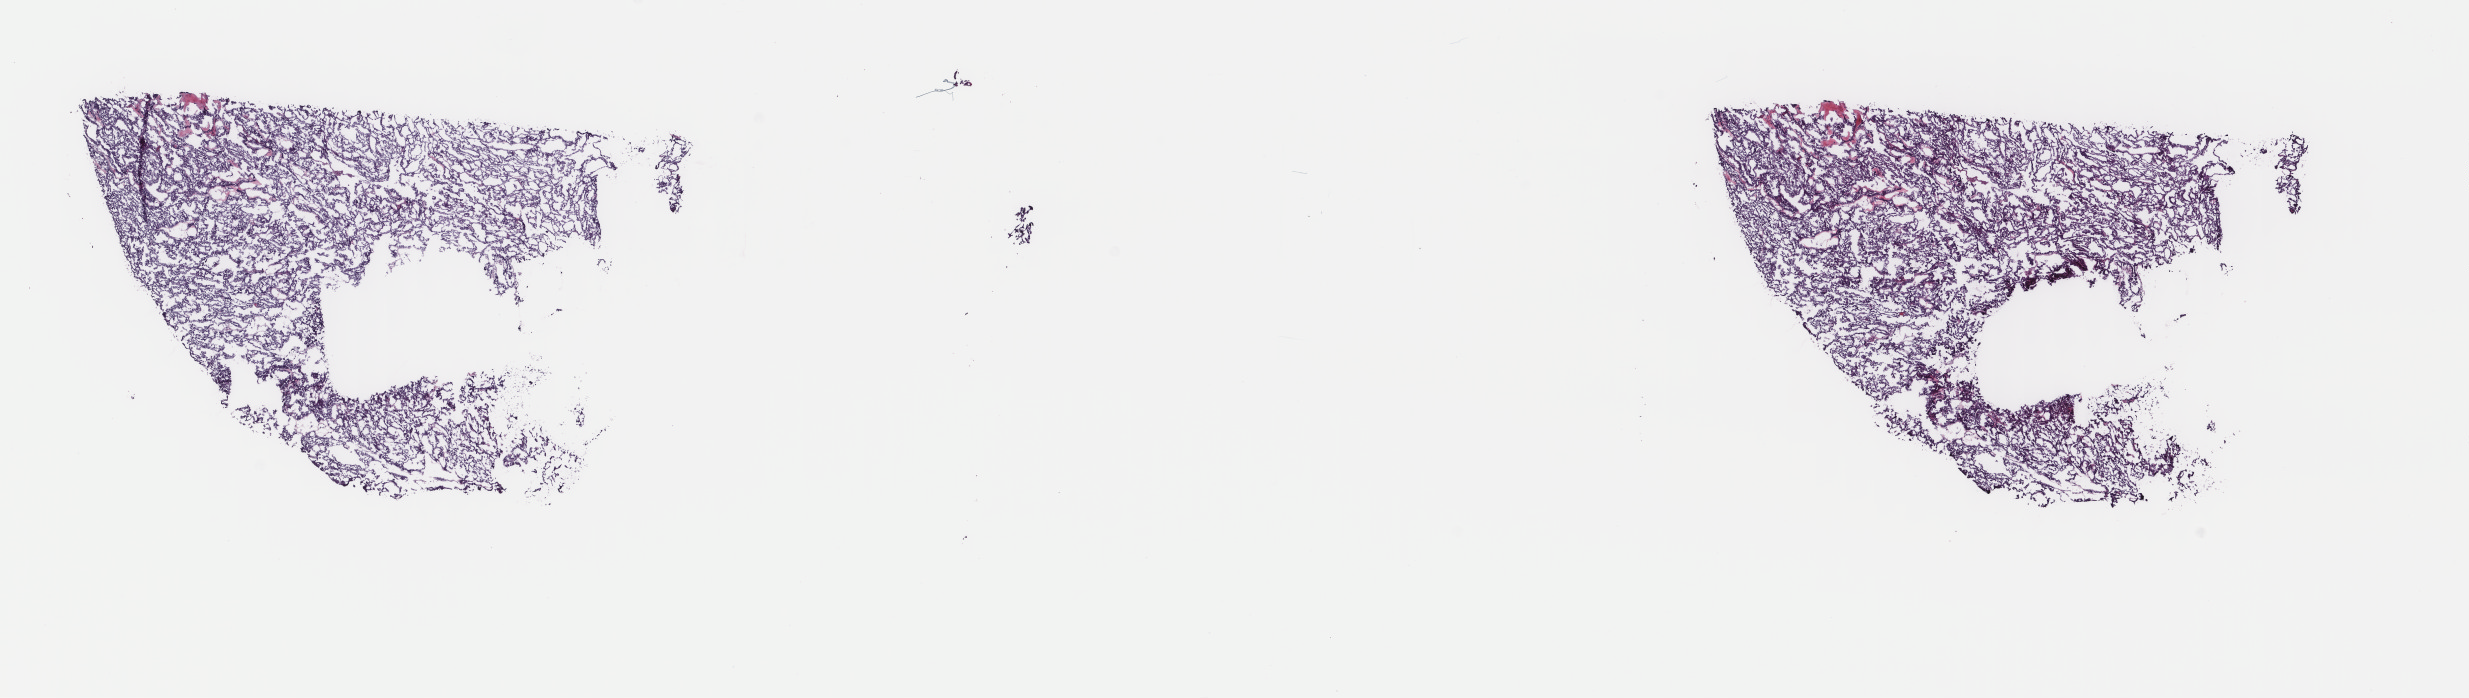
Digitized Hematoxylin and eosin (H&E) stained tissue section (whole slide) — a low-resolution overview of the entire scanned area, about 19.6 x 5.5 mm; frozen section from the top of the tissue portion; thyroid, primary tumour sample. Female patient; age at initial diagnosis 22 years. Slide review estimates, as recorded: tumour cells 85%, tumour nuclei 85%, normal cells 0%, stromal cells 15%, necrosis 0%. Infiltration values recorded for this section: lymphocyte infiltration 0%, monocyte infiltration 0%, neutrophil infiltration 0%.
Lymph nodes positive (case pathology): 0 of 13 examined. Histologic diagnosis: Papillary adenocarcinoma, NOS (thyroid gland). Laterality: right. AJCC pathologic stage: I (6th edition). TNM: T2 N0 M0.